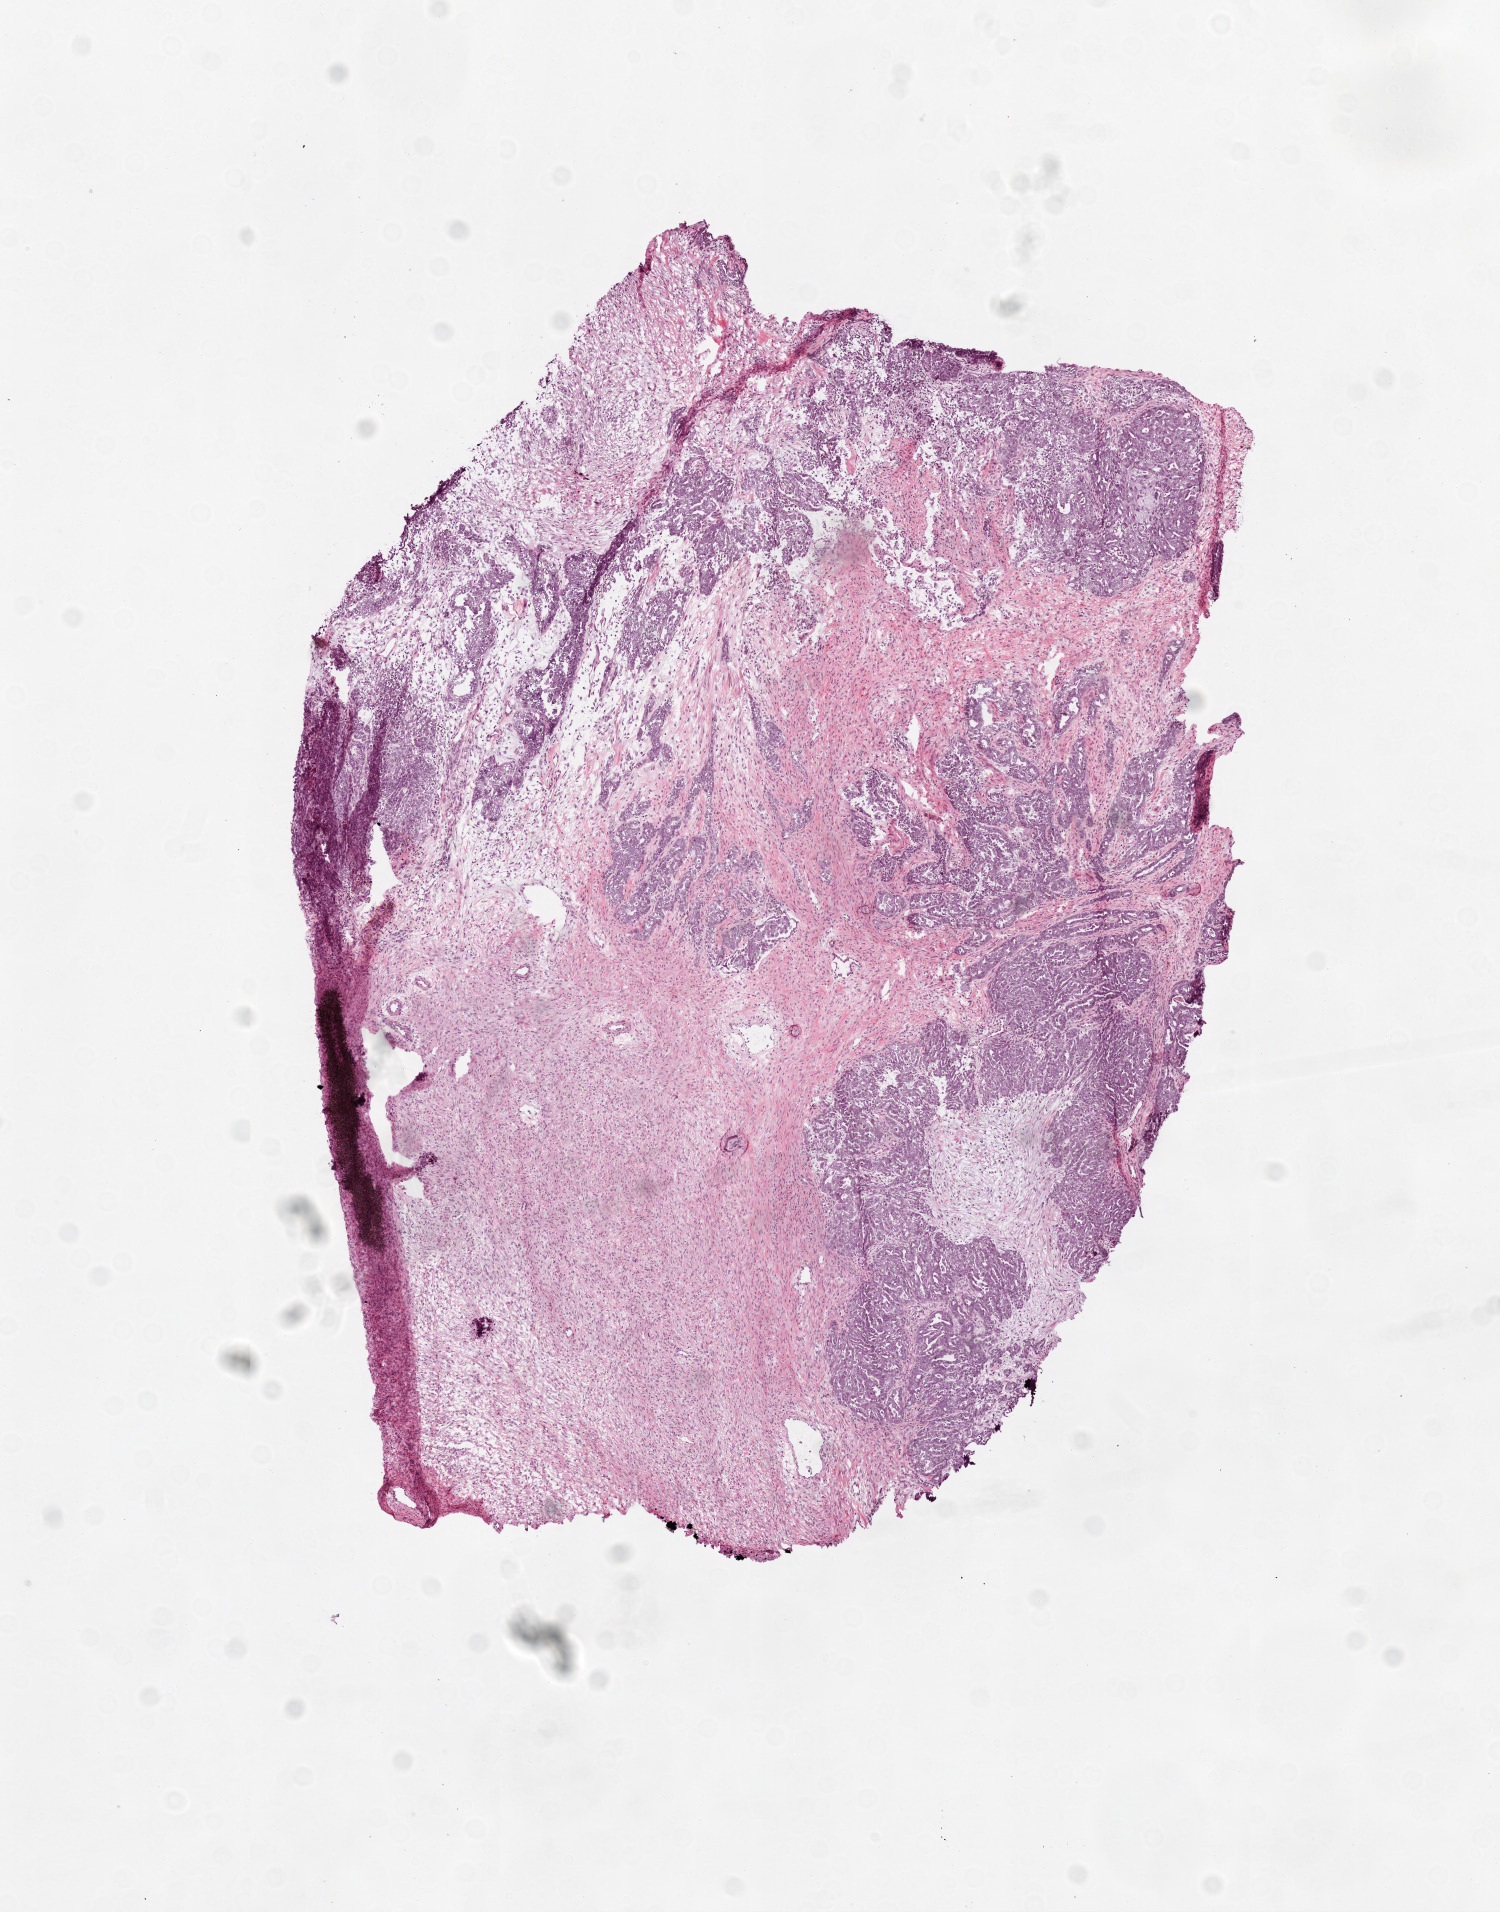
Whole-slide histology image, H&E — a low-resolution overview of the entire scanned area, about 6.0 x 7.7 mm (slide scanned at 20x); frozen section from the top of the tissue portion; ovary, primary tumour sample. Female, age 58 years at initial diagnosis. Histologic grade: G3 (poorly differentiated). Slide review estimates, as recorded: tumour cells 85%, tumour nuclei 85%, normal cells 0%, stromal cells 15%, necrosis 0%.
FIGO stage: IV. Diagnosis: Serous cystadenocarcinoma, NOS. Laterality: right.